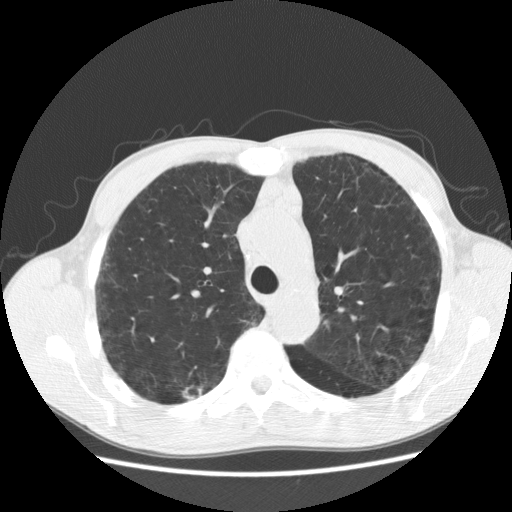
Low-dose screening chest CT, axial slice; second annual screen; lung window (W 1500 / L -600 HU); 120 kVp; slice 137 of 195 in the series; 512 × 512 image matrix. Male participant, aged 60 years at enrolment. Current smoker at enrolment.
• Expert reader's lesion annotation, box from (x=170, y=375) to (x=212, y=407) px.
• The exam's reader record, not a measurement of the box and not confirmed to be the same lesion: non-calcified nodule or mass ≥4 mm, right upper lobe, 8 × 5 mm, poorly defined margins, soft tissue attenuation, pre-existing on the prior screen: yes; interval growth: yes.
• Official screen result: positive, other.
• Participant outcome: lung cancer diagnosed 204 days after this screen — squamous cell carcinoma, NOS, right upper lobe, well differentiated (G1), stage IA (AJCC 6th edition), 15 mm at pathology.